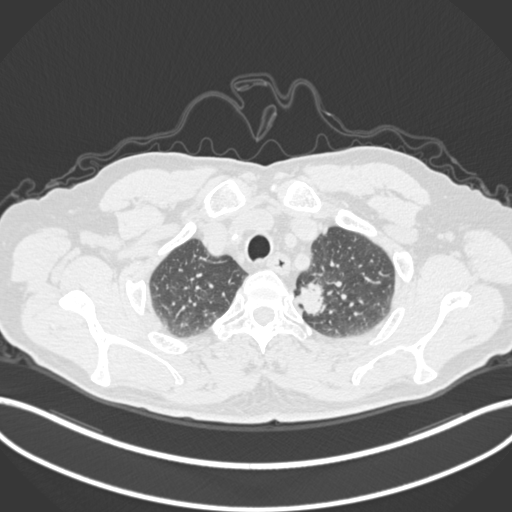
Chest CT, one axial slice. Position 276 of 306 along the scan axis. 120 kVp. Lung window (W 1500 / L -600 HU). 512 × 512 image matrix, field of view 400 × 400 mm. Male patient, age 64 years. Case-level facts recorded for this patient, not image findings: clinical TNM (as recorded): T1c N0 M0.
Structures marked on this image (bounding box drawn by a radiologist):
- lung tumour (recorded histology: adenocarcinoma): box from (x=296, y=278) to (x=330, y=317) px